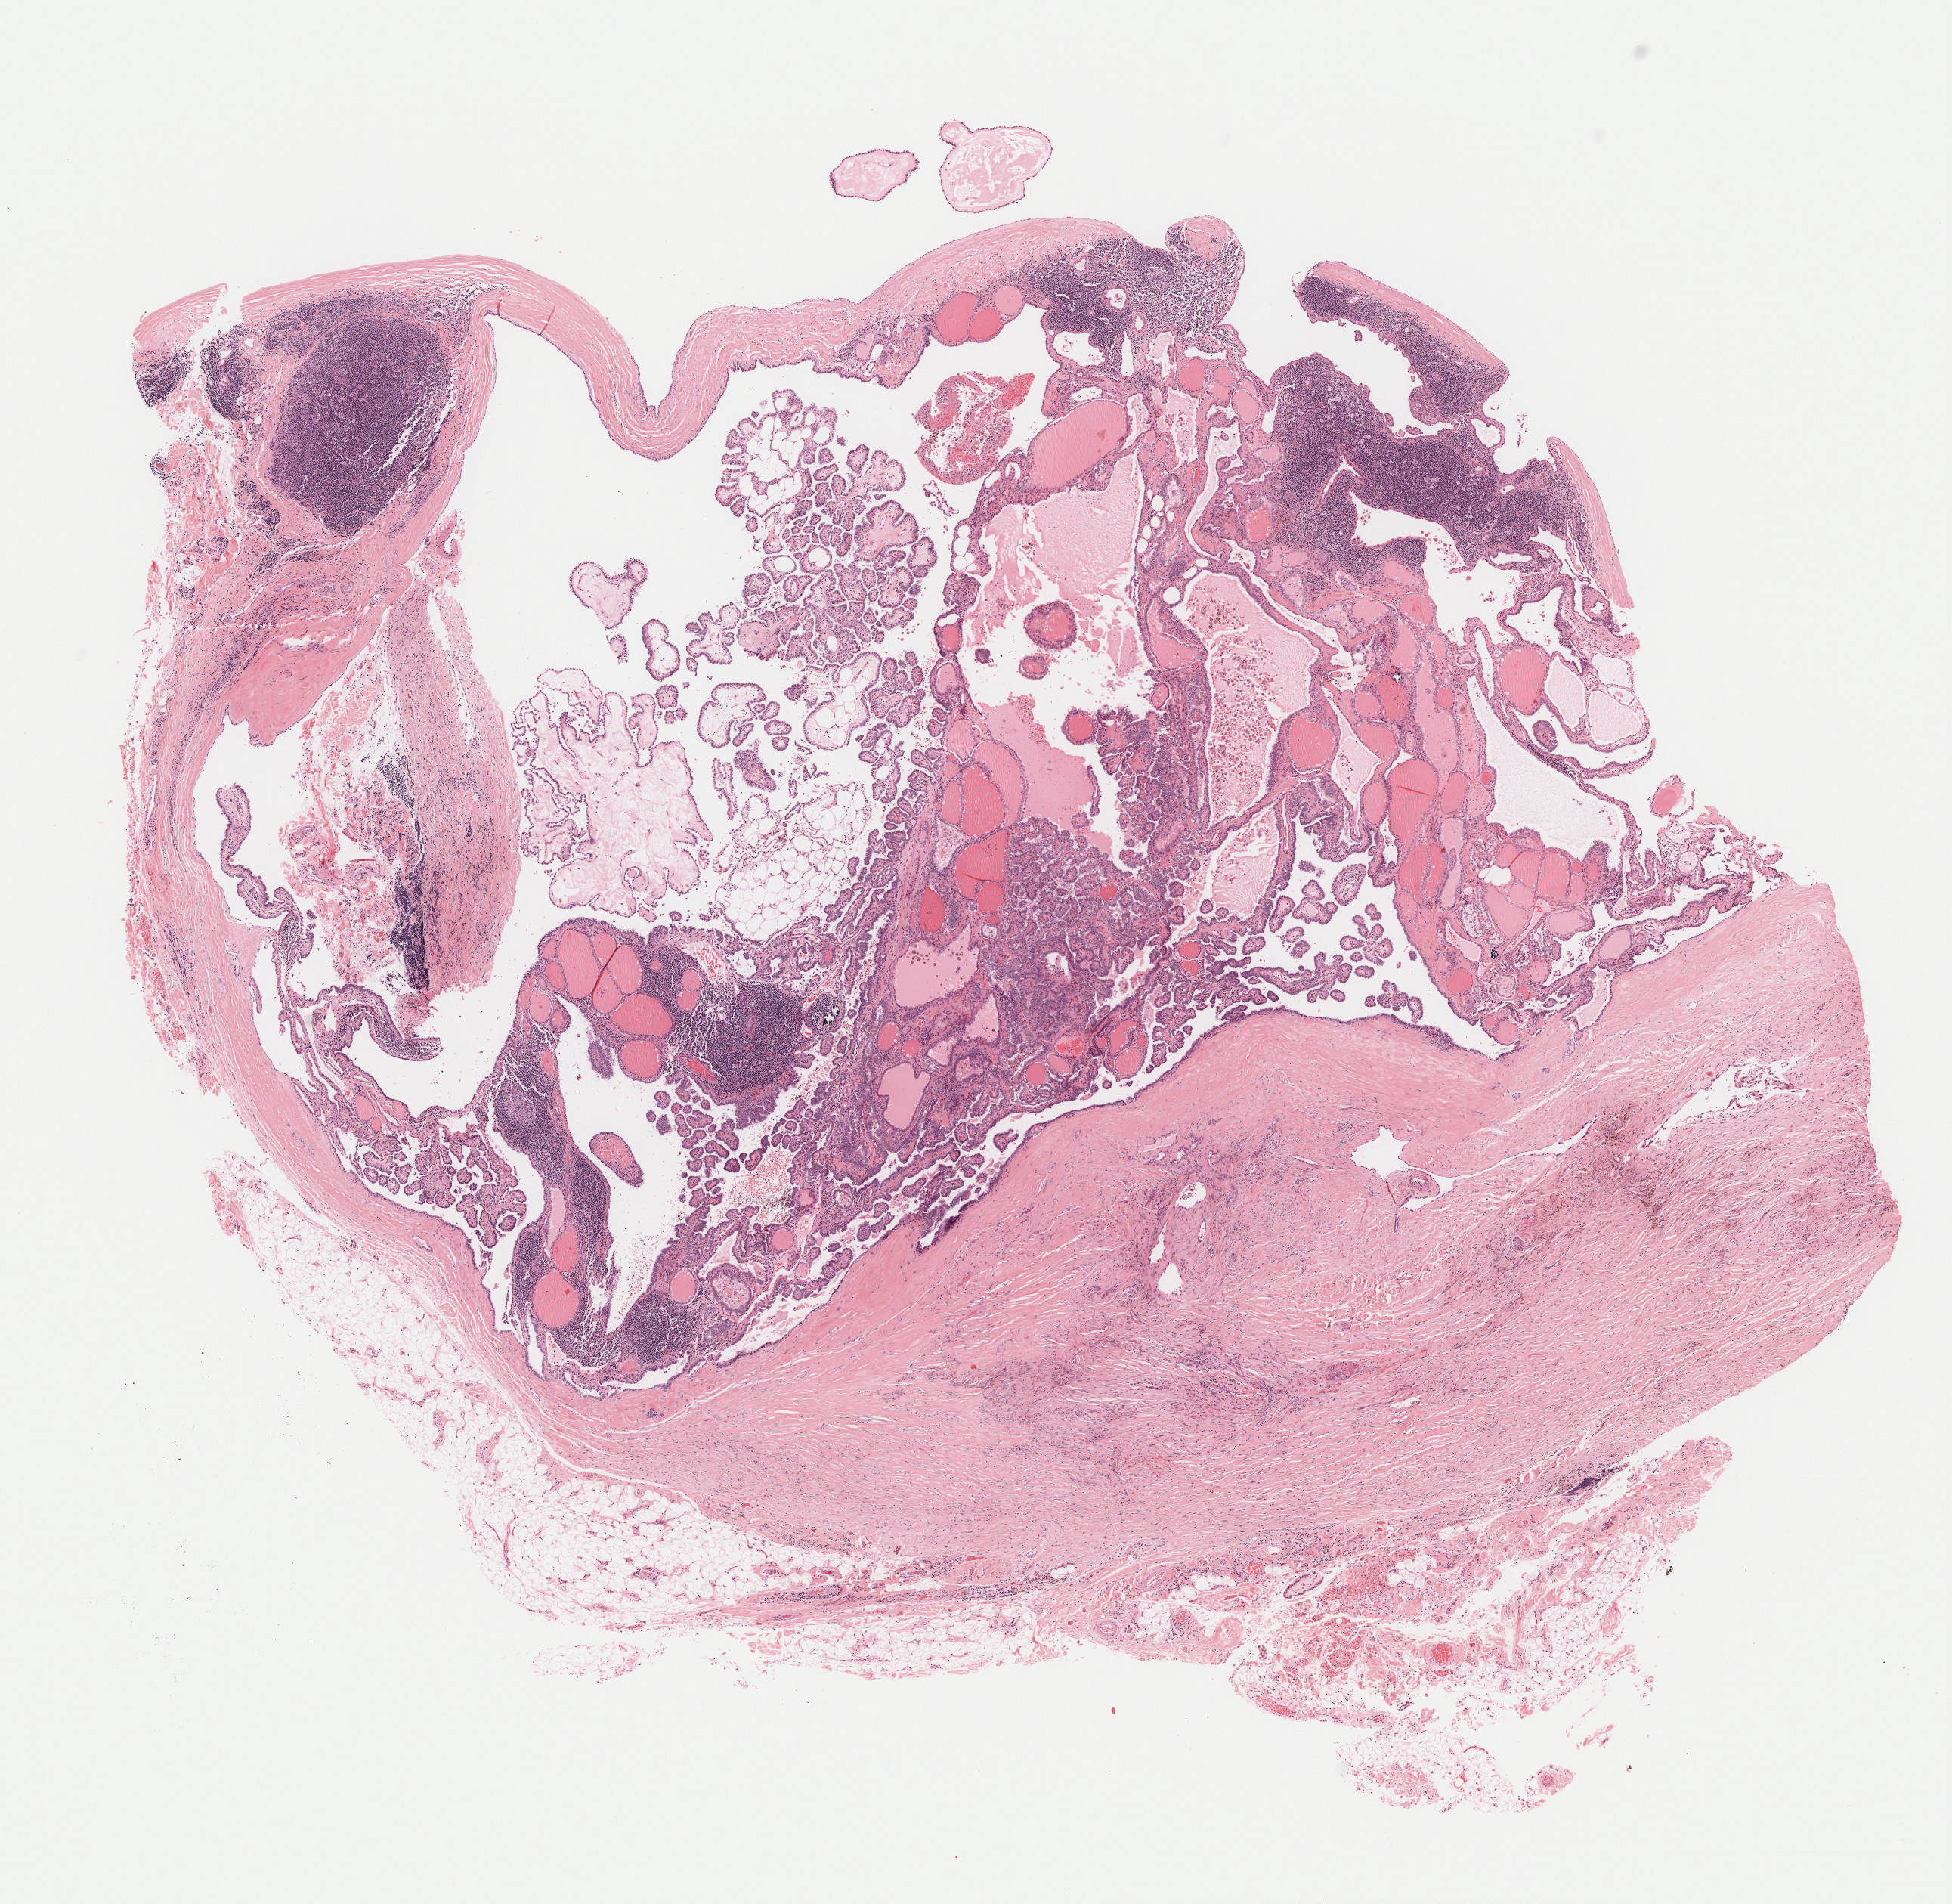
Digitized H&E-stained tissue section (whole slide), whole scanned area (about 10.4 x 10.1 mm) shown as a low-resolution overview; formalin-fixed paraffin-embedded (FFPE) diagnostic section; thyroid, primary tumour sample. Male, age 33 years at initial diagnosis.
Pathologic diagnosis: Papillary adenocarcinoma, NOS (thyroid gland).